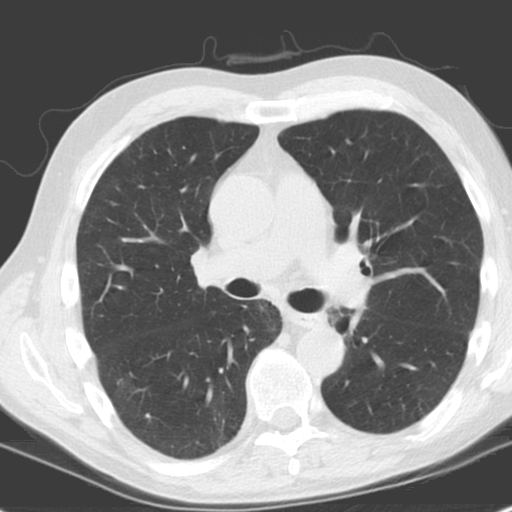
Chest CT (low-dose screening protocol), one axial image, baseline annual screen, lung window (W 1500 / L -600 HU), standard (soft-tissue) reconstruction kernel (C), 120 kVp, slice 76 of 185 in the series, 512 × 512 image matrix. Male, age 61 years at enrolment.
Expert-annotated lung lesion, box from (x=309, y=302) to (x=353, y=341) px. No non-calcified nodule or mass ≥4 mm was recorded by the screening reader at this exam. Participant outcome: lung cancer diagnosed 1146 days after this screen (after the third annual screen) — squamous cell carcinoma, NOS, left upper lobe, left lower lobe, well differentiated (G1), stage IIB (AJCC 6th edition), 100 mm at pathology.